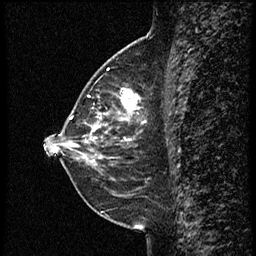
Breast MRI (dynamic contrast-enhanced), one sagittal slice. Slice 25 of 60 in the series (ordered by position). Dynamic contrast-enhanced study with each time point stored as its own series, time point 2 of 3 at this slice position (early post-contrast, ordered by acquisition time). 1.5 T. TE 4.2 ms, TR 18.9 ms. 256 × 256 image matrix, field of view 200 × 200 mm. Female patient. From the clinical record (not read from this slice): setting: breast cancer imaged before/during neoadjuvant chemotherapy; receptor status: HER2-positive.
Outlined on this slice (semi-automatic segmentation, software-assisted and operator-edited):
- analysis volume of interest (the breast-tissue region the enhancement analysis was run in; not a lesion): bounding box [x1, y1, x2, y2] px = [77, 82, 157, 147]
- tumour enhancement mask (voxels above the 100 % enhancement threshold inside the analysis volume of interest): [77, 90, 141, 147]